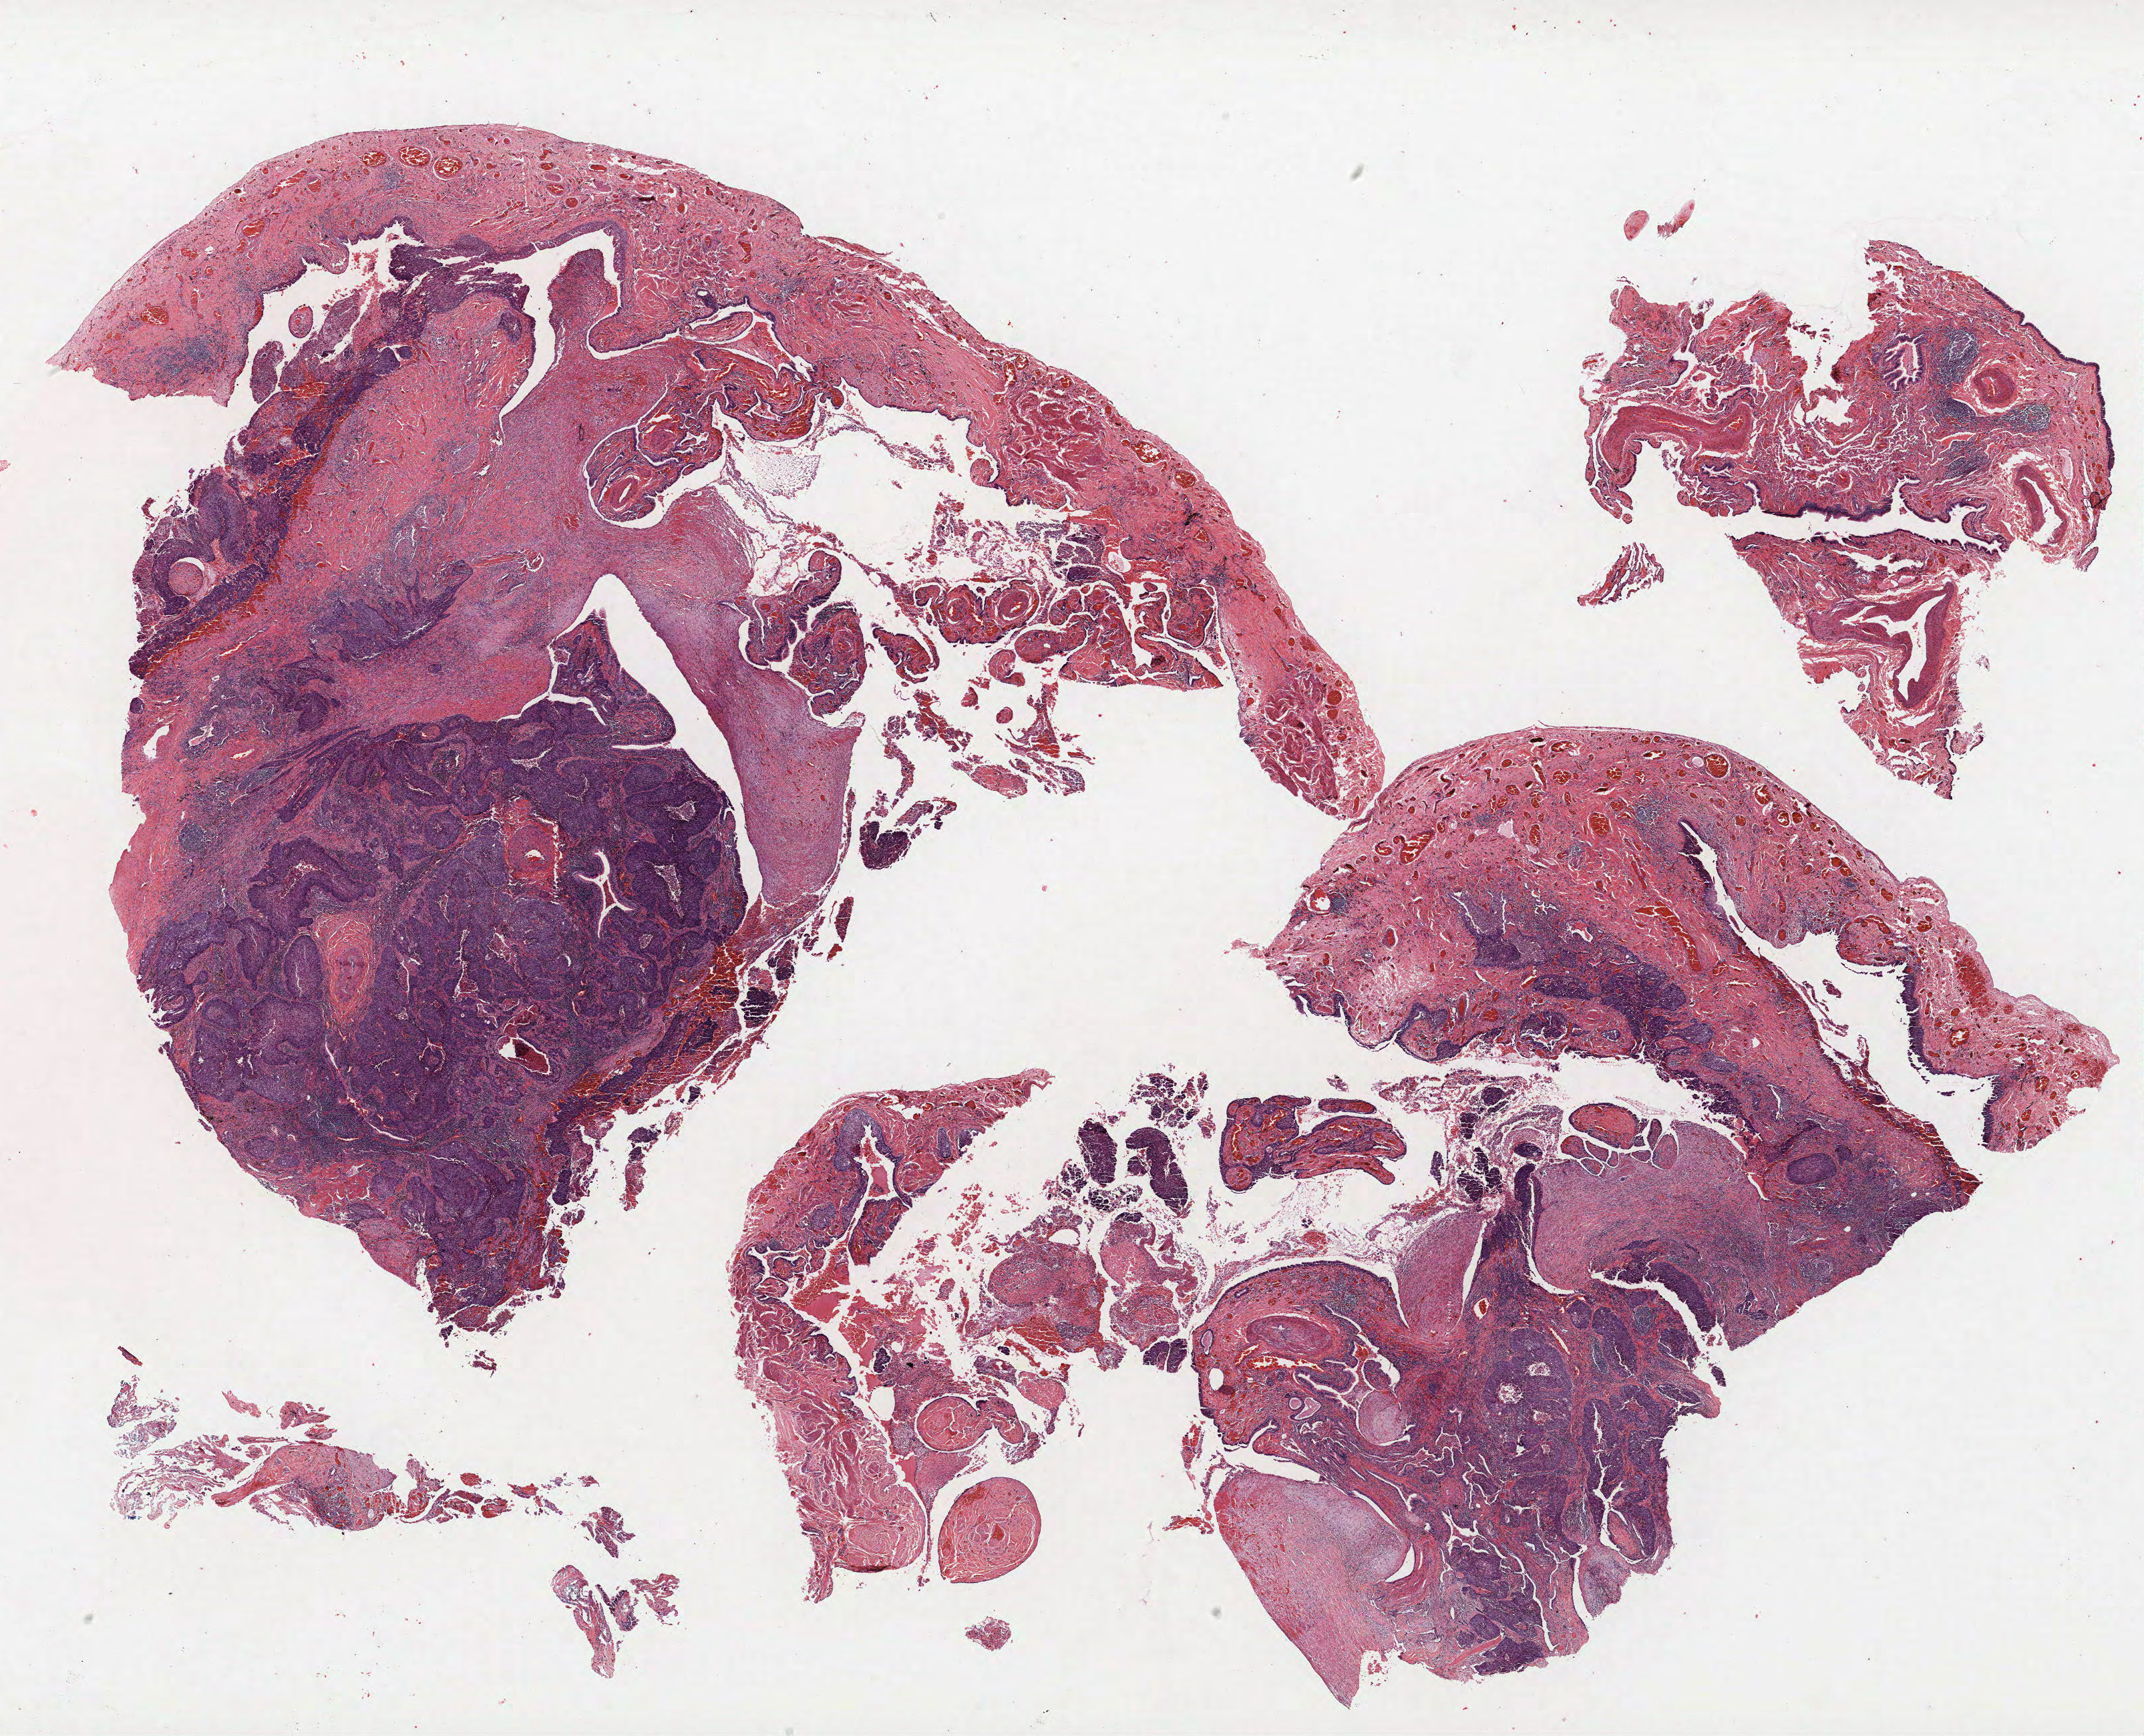
H&E-stained whole-slide image — a low-resolution overview of the entire scanned area, about 25.7 x 20.8 mm (acquisition: 40x scan). Formalin-fixed paraffin-embedded (FFPE) section. Lung. Male, age 58 at enrolment. Grade: moderately differentiated (G2).
• stage (AJCC 6th edition): IB
• participant's lung-cancer diagnosis: Squamous cell carcinoma, keratinizing, NOS
• tumour size (pathology): 38 mm
• primary tumour location (clinical record): right lower lobe
• note: participant had 2 primary lung cancers recorded; fields above describe the first